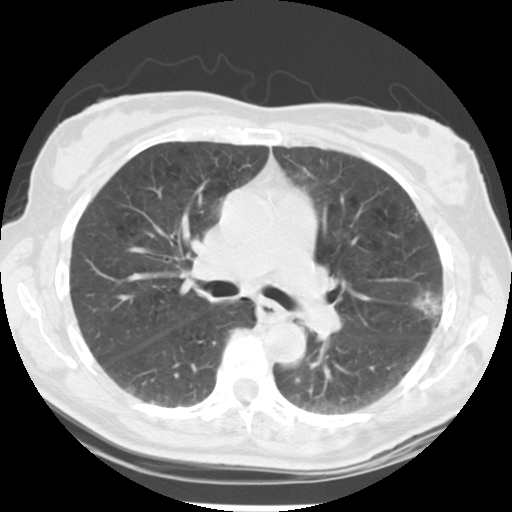
Low-dose screening chest CT, one axial slice; reconstruction kernel STANDARD; 120 kVp; lung window (W 1500 / L -600 HU); 2.5 mm slice thickness; 512 × 512 image matrix, field of view 302 × 302 mm.
Structures marked on this image (outlined manually by an expert reader):
- lesion 1 (tumor, upper lobe of left lung): bounding box [x1, y1, x2, y2] px = [413, 292, 442, 319]